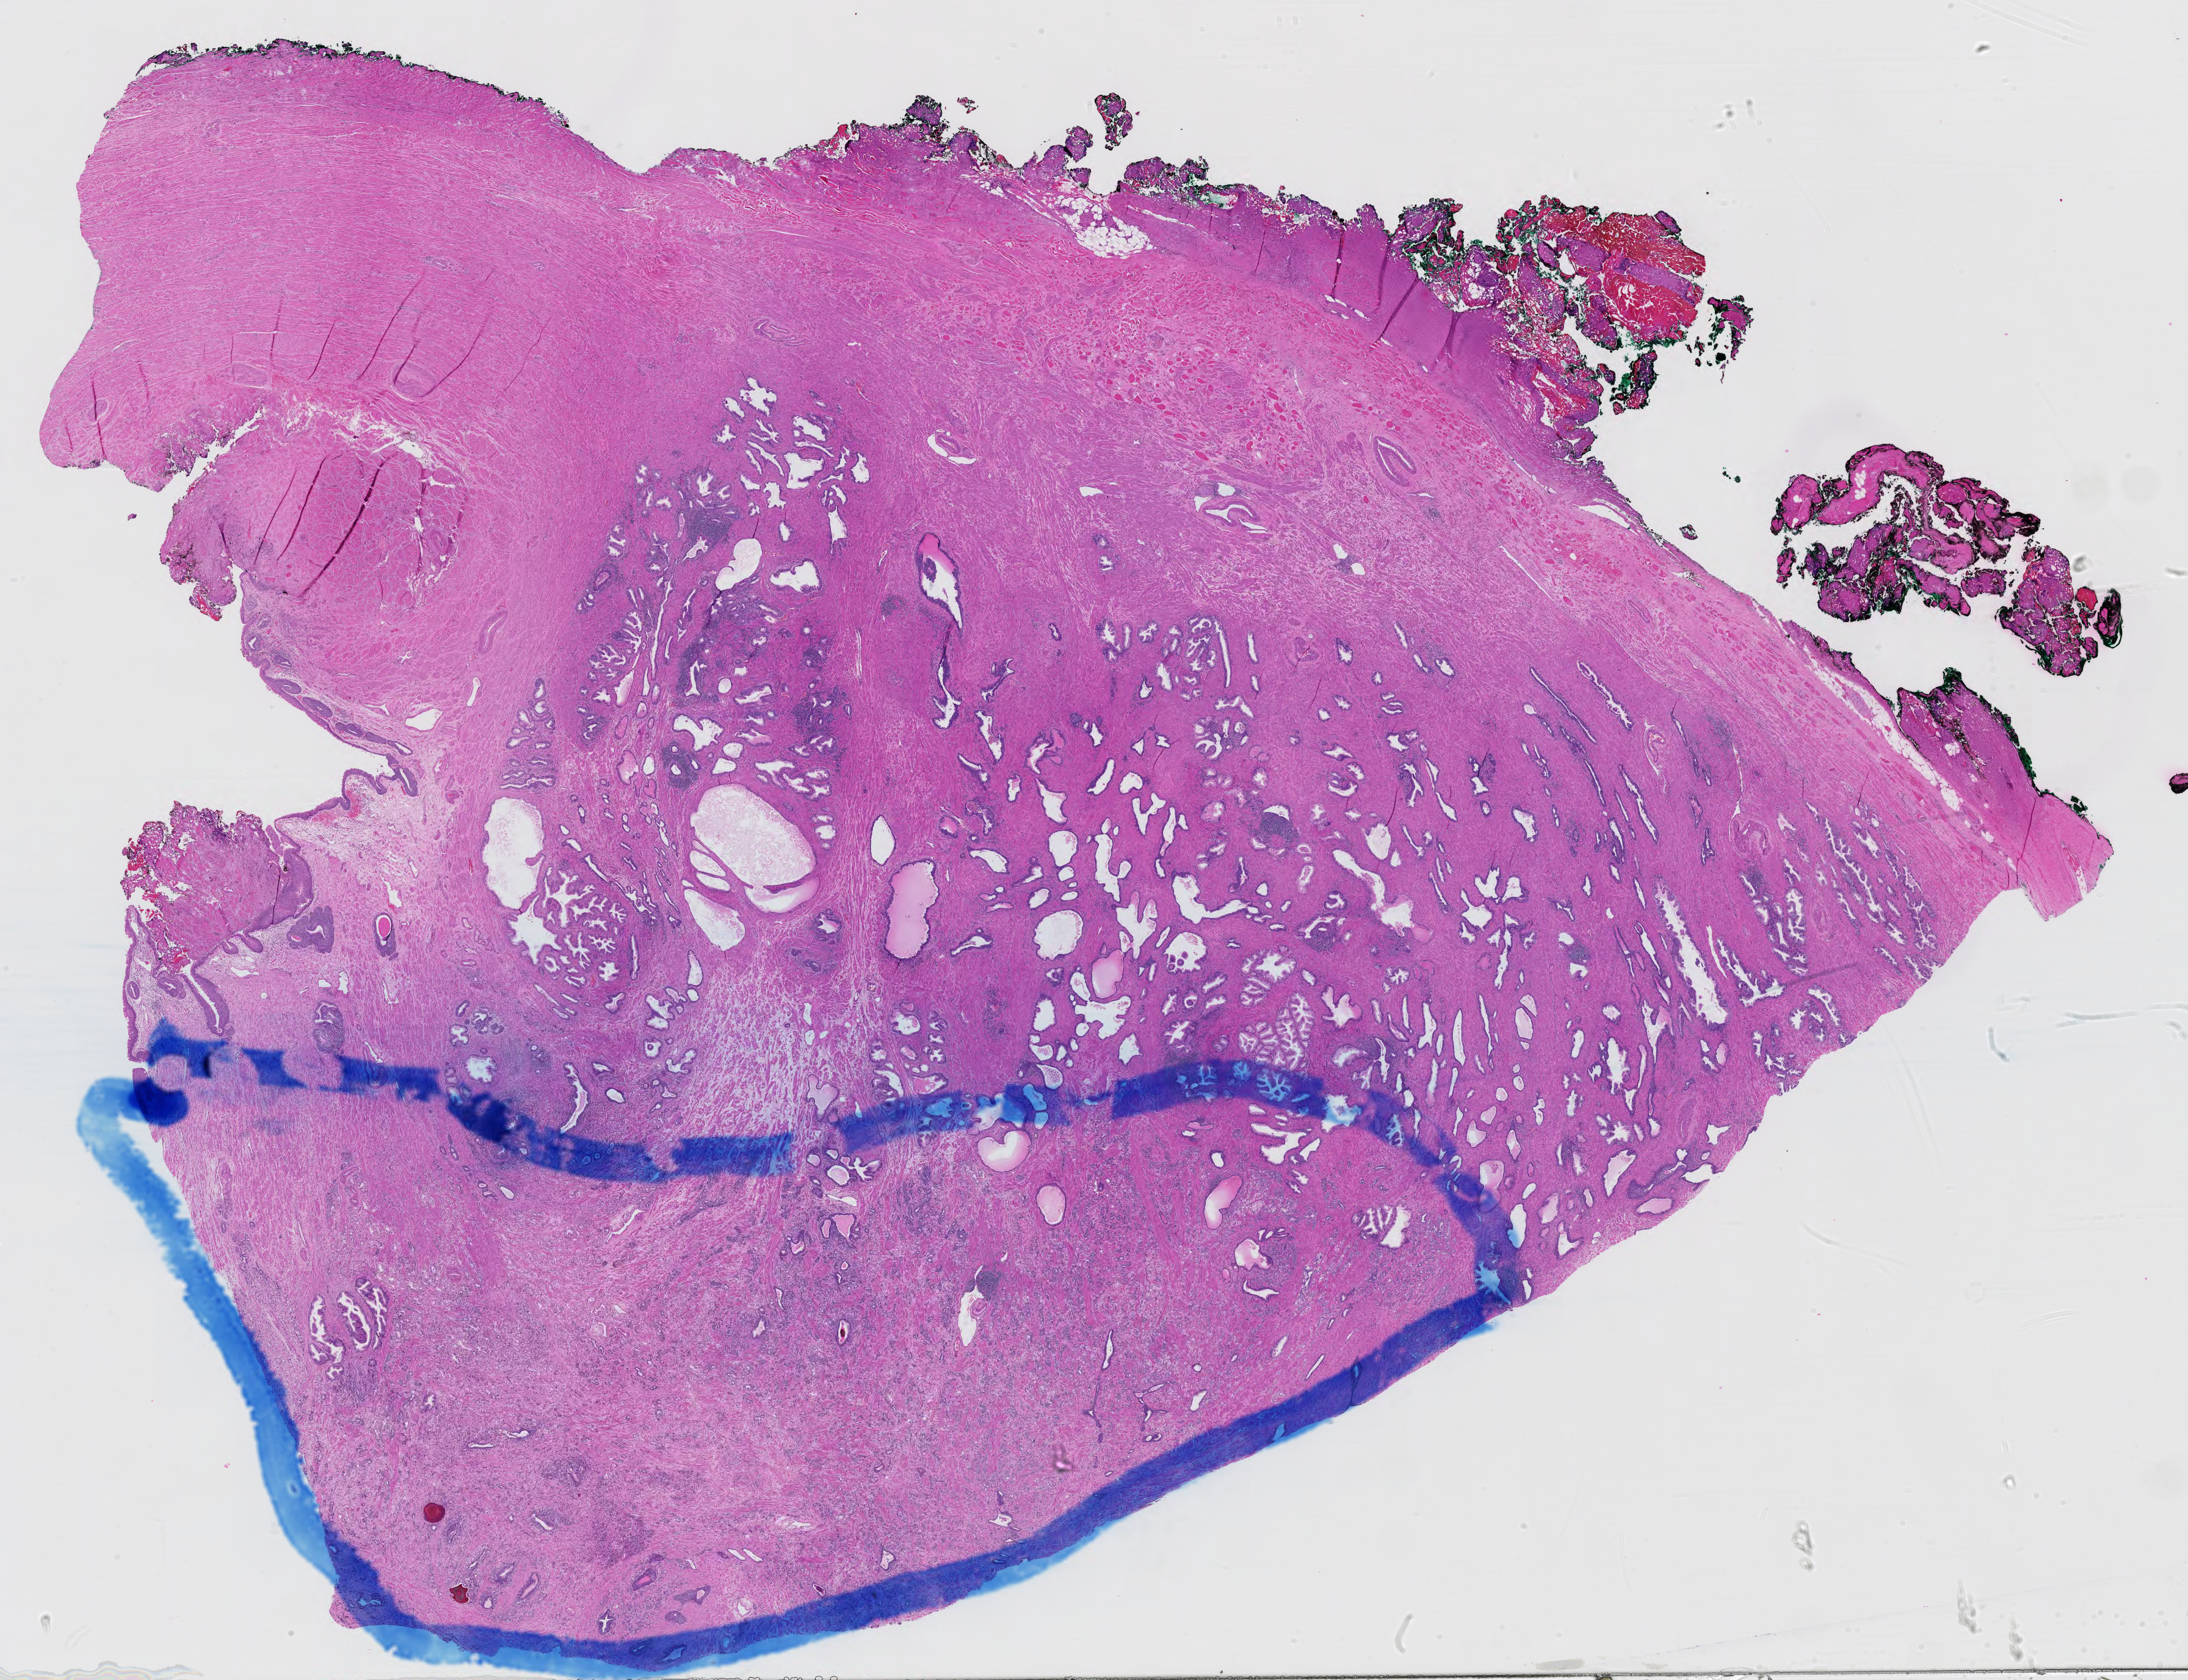
Digitized Hematoxylin and eosin (H&E) stained tissue section (whole slide) — whole scanned area (about 26.0 x 20.0 mm) shown as a low-resolution overview. Formalin-fixed paraffin-embedded (FFPE) diagnostic section. Prostate, primary tumour sample. Patient: male, age at initial diagnosis 60 years. Gleason score: 9 (4+5).
Laterality: bilateral. Pathologic diagnosis: Adenocarcinoma, NOS.